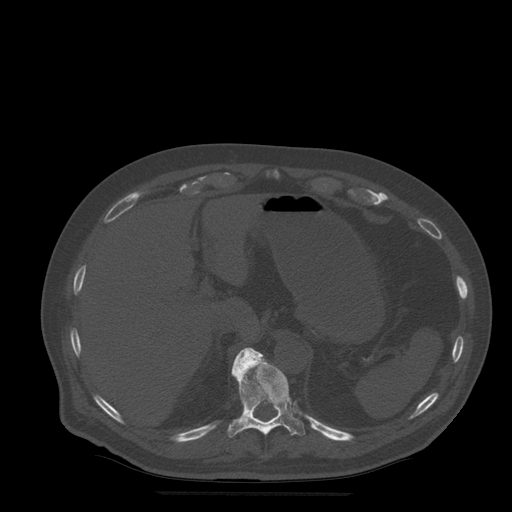
CT including the spine, one axial slice. Position 246 of 522 along the scan axis. Bone window (W 1800 / L 400 HU). 512 × 512 image matrix, field of view 420 × 420 mm. Patient age 72 years. Case-level facts recorded for this patient, not image findings: primary cancer: prostate.
Annotated regions visible in this slice (semi-automatically segmented with operator editing):
- T11 vertebra: bounding box (x1, y1, x2, y2) in pixels: (227, 348, 305, 438)